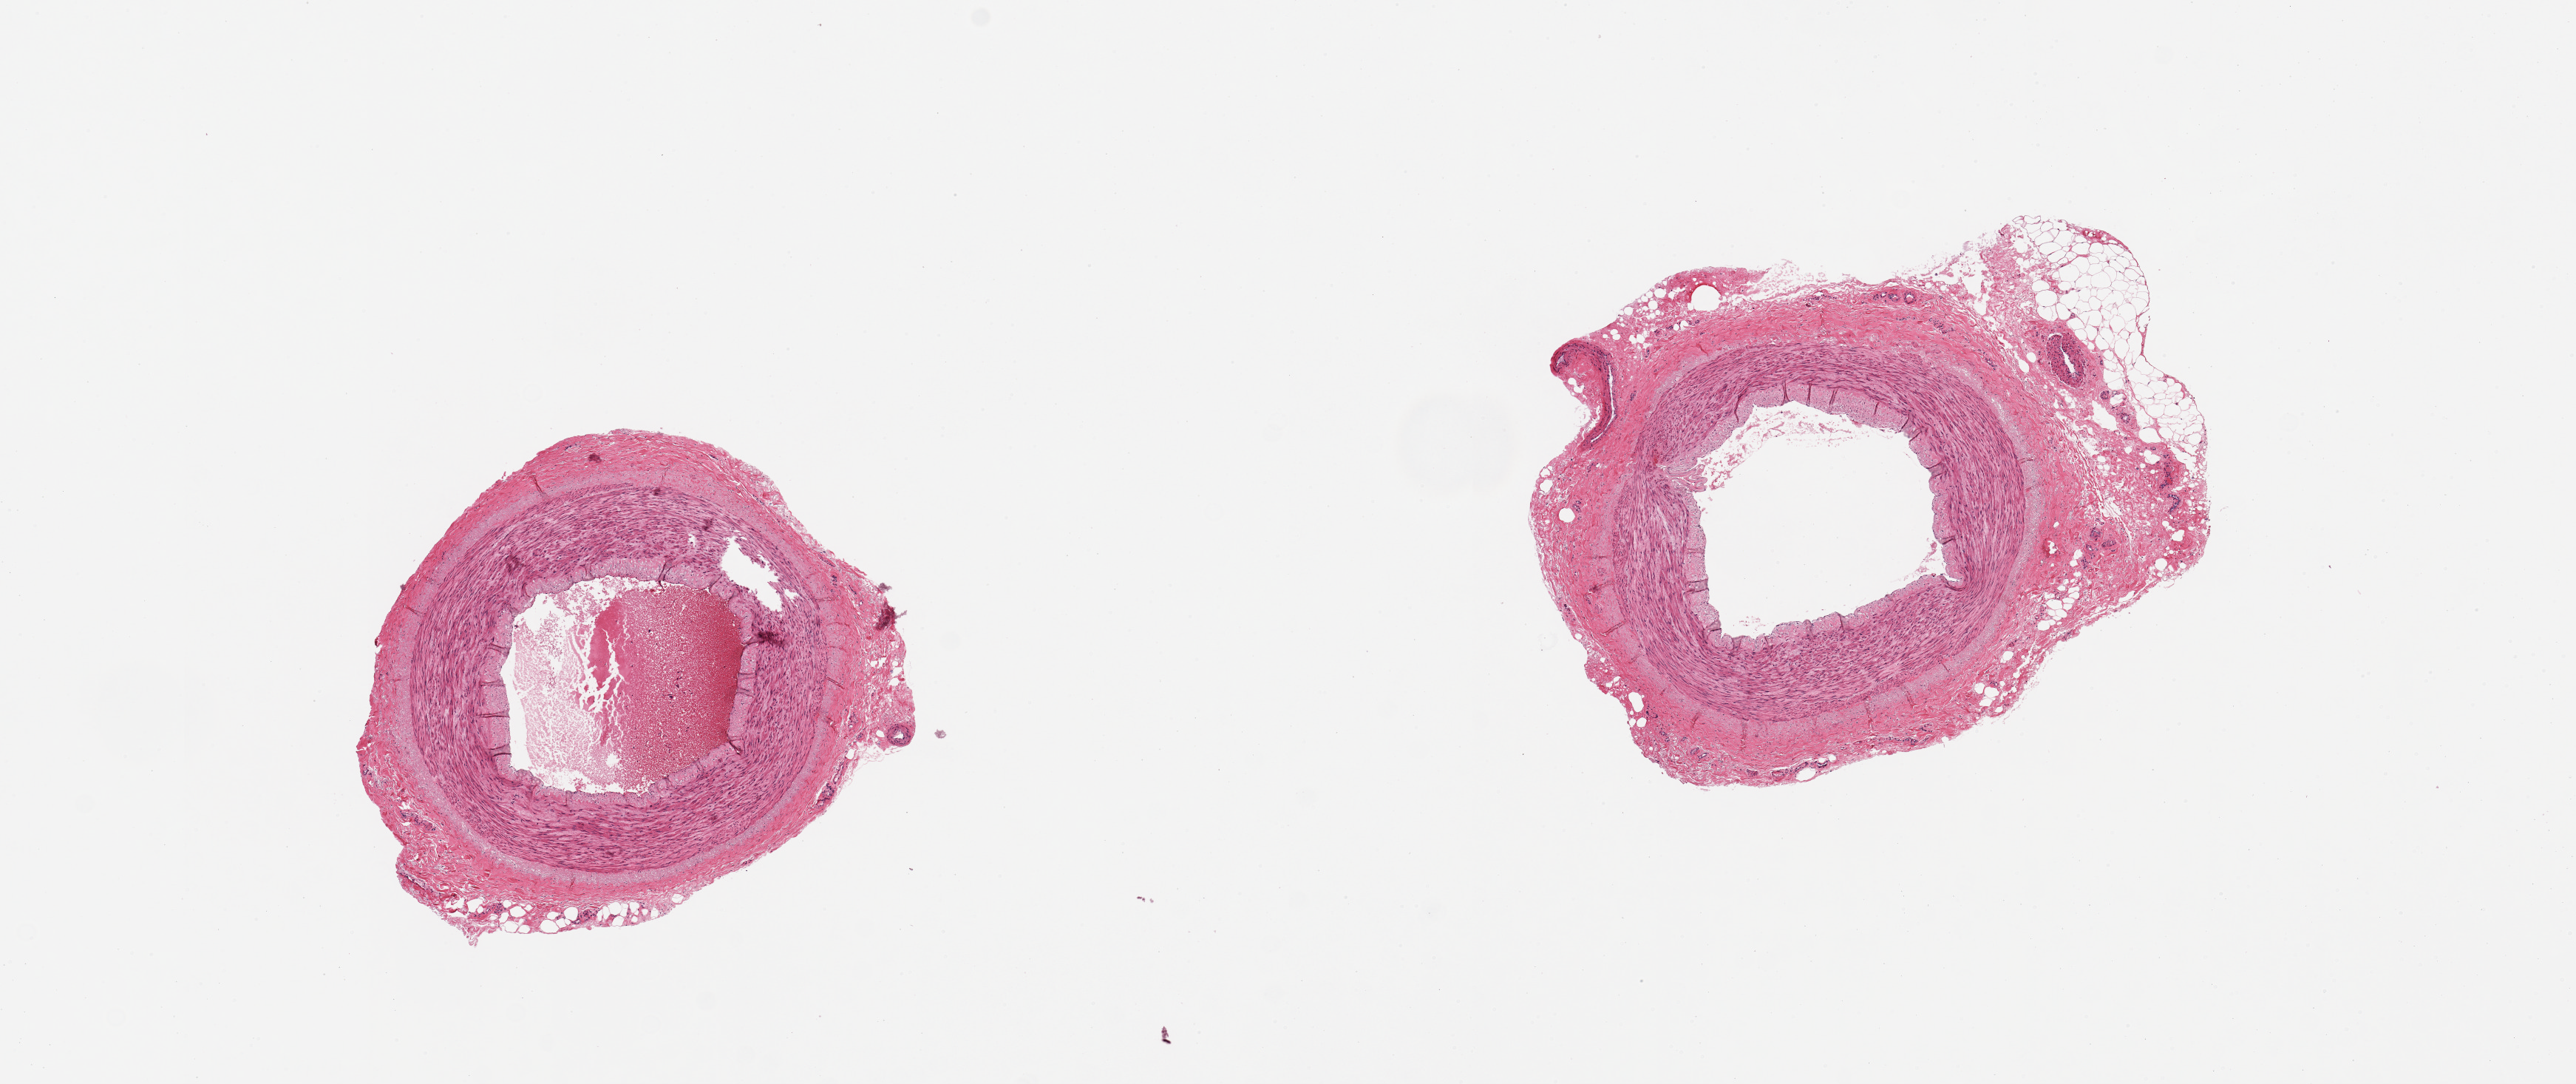
Digitized hematoxylin and eosin (H&E)-stained section, brightfield, whole scanned area (about 13.8 x 5.8 mm) shown as a low-resolution overview; PAXgene-fixed paraffin-embedded (PFPE) section; section of tibial artery (target tissue); donor tissue sample. Female donor.
- review note (as recorded): 2 pieces, 3x2.5 & 4x3mm; one aliquot has ~0.5mm nubbin of adherent fat/fibrous tissue